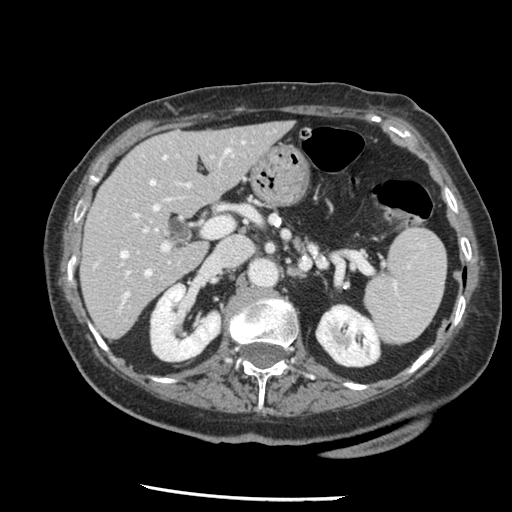
Contrast-enhanced abdominal CT, one axial slice. Position 77 of 148 along the scan axis. 120 kVp. Intravenous contrast given. Soft-tissue window (W 400 / L 40 HU). 2.5 mm slice thickness. 512 × 512 image matrix, field of view 330 × 330 mm. Female patient, age 85 years. From the clinical record (not read from this slice): diagnosis: colorectal cancer liver metastases, imaged before liver resection; multiple liver metastases: no; largest metastasis: 0.9 cm; disease in both lobes: no.
Annotated regions visible in this slice (manually delineated by an expert):
- hepatic veins: bounding box [x1, y1, x2, y2] px = [121, 142, 183, 301]
- liver: [82, 123, 290, 338]
- planned liver remnant (the part of the liver to remain after resection): [82, 123, 290, 338]
- portal vein (with intrahepatic branches): [125, 147, 230, 277]